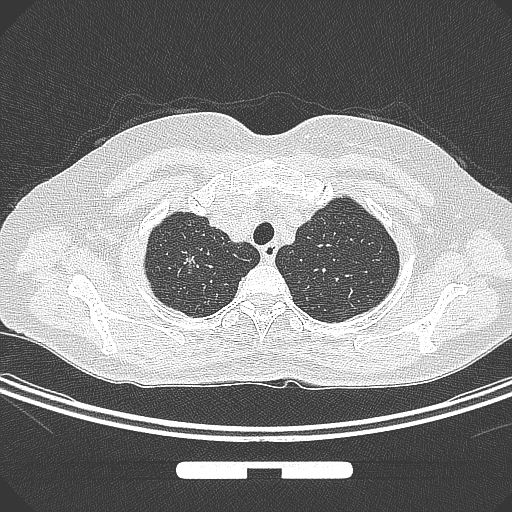
Chest CT, one axial slice; position 254 of 295 along the scan axis; 120 kVp; lung window (W 1500 / L -600 HU); 1 mm slice thickness; 512 × 512 image matrix, field of view 369 × 369 mm. Female patient, age 58 years. Case-level facts recorded for this patient, not image findings: clinical TNM (as recorded): T1b N0 M0.
Outlined on this slice (bounding box drawn by a radiologist):
- lung tumour (recorded histology: adenocarcinoma): box from (x=175, y=252) to (x=200, y=272) px